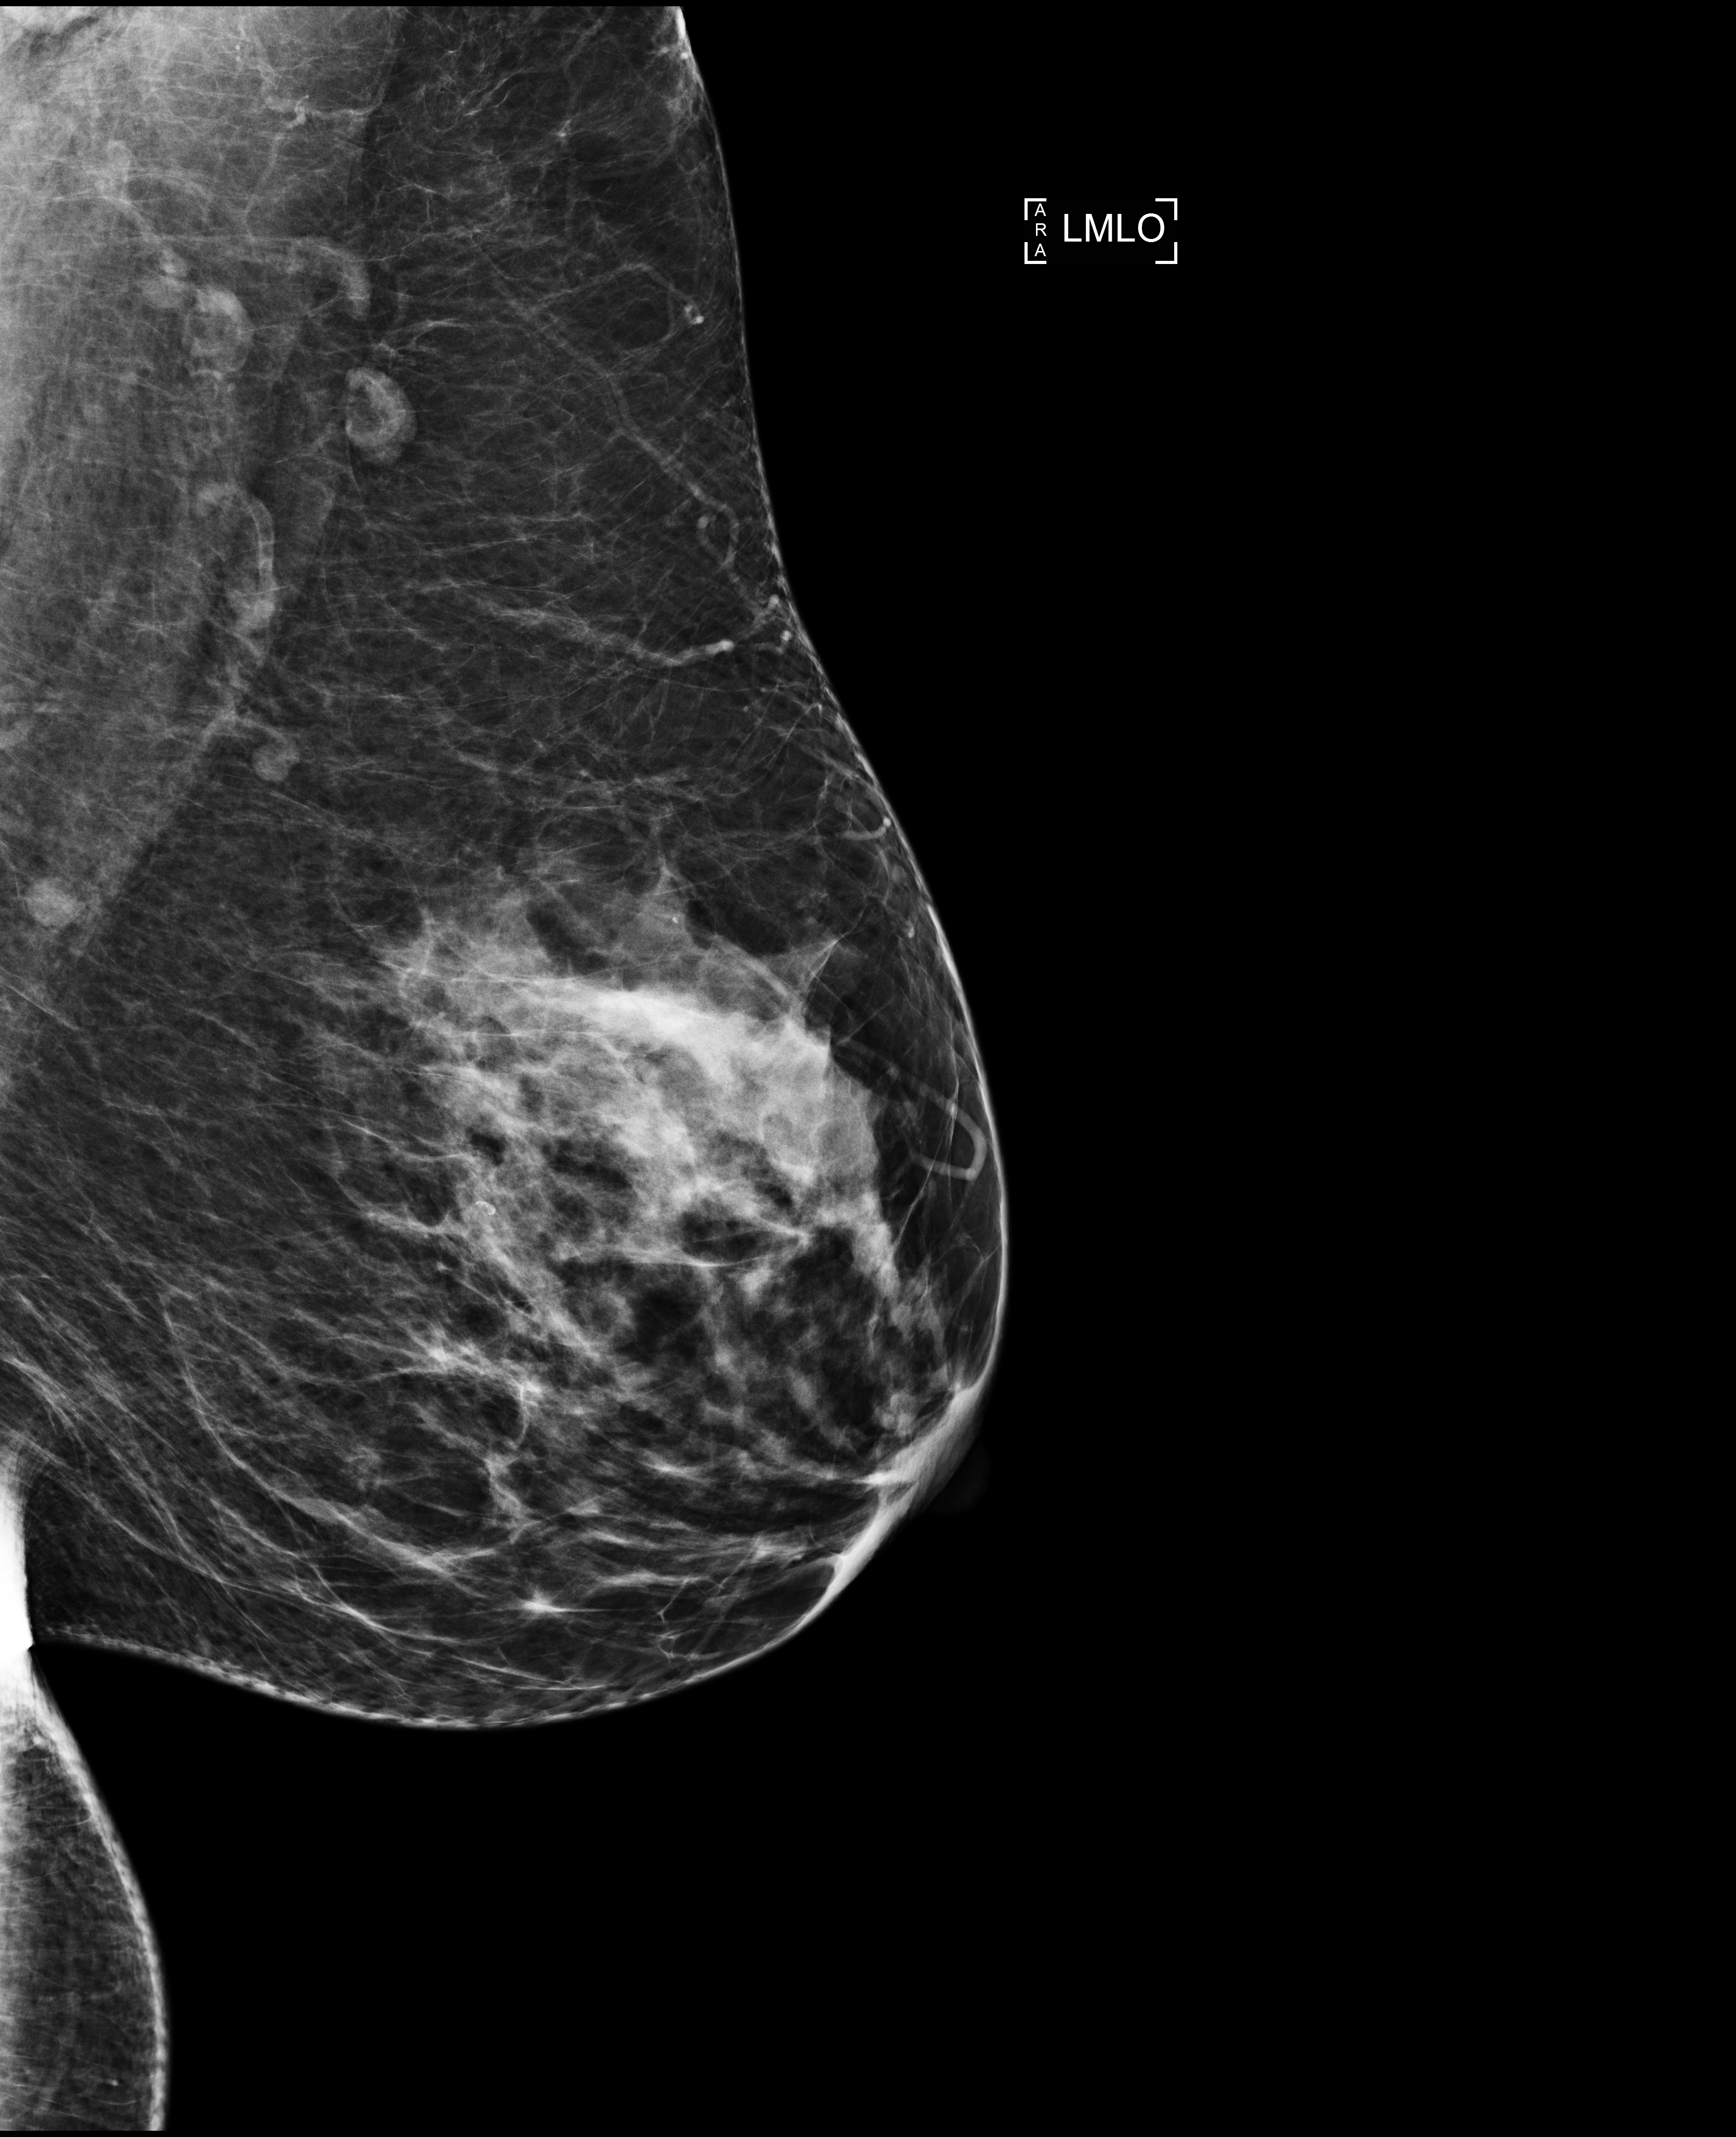
Full-field digital mammogram (FFDM), left breast, mediolateral oblique (MLO) view, annual screening mammography examination, compressed breast thickness 70 mm, system: Selenia Dimensions. Female patient, age 51 years.
Final BI-RADS assessment for this screening round (tomosynthesis exam, both breasts): category 1.